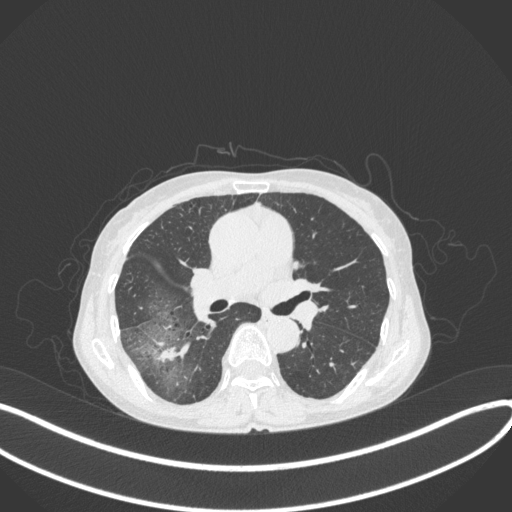
Chest CT, one axial slice. Slice 225 of 379 in the series (ordered by position). Reconstruction kernel B31f. Lung window (W 1500 / L -600 HU). 1 mm slice thickness. 512 × 512 image matrix, field of view 400 × 400 mm. Female patient, age 69 years. Case-level facts recorded for this patient, not image findings: clinical TNM (as recorded): T1b N0 M0; histopathological grade: G2-3.
Structures marked on this image (bounding box drawn by a radiologist):
- lung tumour (recorded histology: adenocarcinoma): bounding box (x1, y1, x2, y2) in pixels: (152, 340, 194, 366)